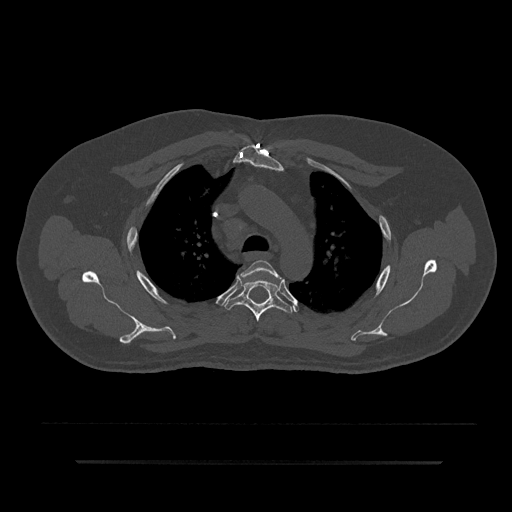
CT including the spine, one axial slice. Slice 626 of 797 in the series (ordered by position). Bone window (W 1800 / L 400 HU). 512 × 512 image matrix, field of view 464 × 464 mm. Male patient, age 59 years. From the clinical record (not read from this slice): primary cancer: bile ducts; vertebrae with lytic lesions (as recorded): T10.
Outlined on this slice (semi-automatically segmented with operator editing):
- T3 vertebra: box from (x=241, y=260) to (x=283, y=281) px
- T4 vertebra: (x=223, y=272)–(x=294, y=322)